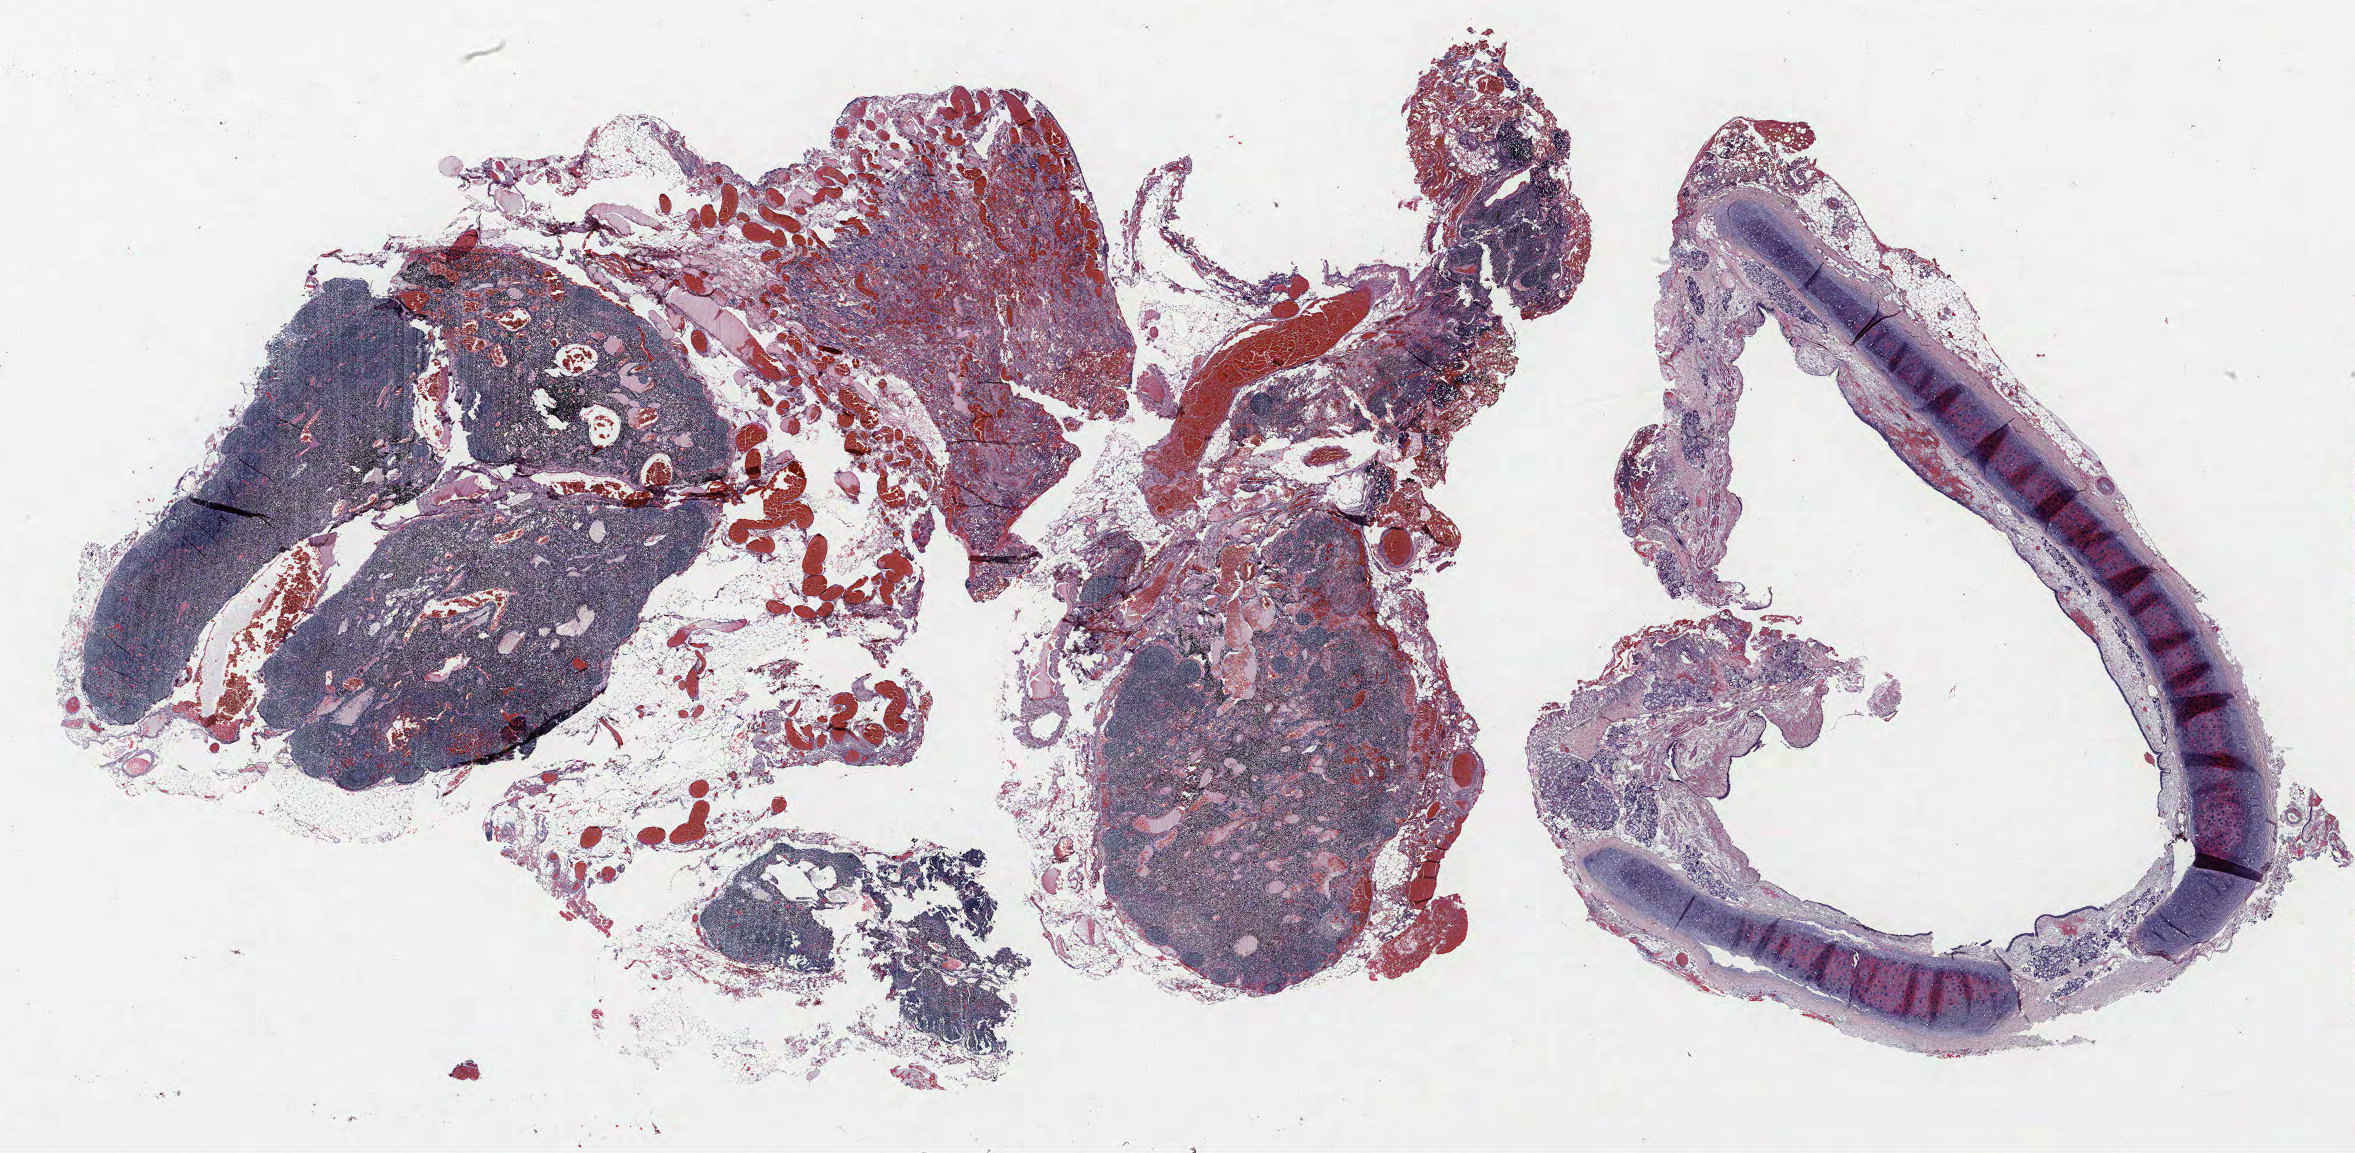
Hematoxylin and eosin (H&E) stained whole-slide image, shown as a low-resolution overview of the whole scanned area (about 37.7 x 18.5 mm), formalin-fixed paraffin-embedded (FFPE) section, lung tissue. Female patient, aged 65 at enrolment. Former smoker at enrolment. Grade: moderately differentiated (G2).
- stage (AJCC 6th edition): IIB
- tumour size (pathology): 90 mm
- participant's lung-cancer diagnosis: Squamous cell carcinoma, NOS (ICD-O-3 8070/3)
- primary tumour location (clinical record): left lower lobe